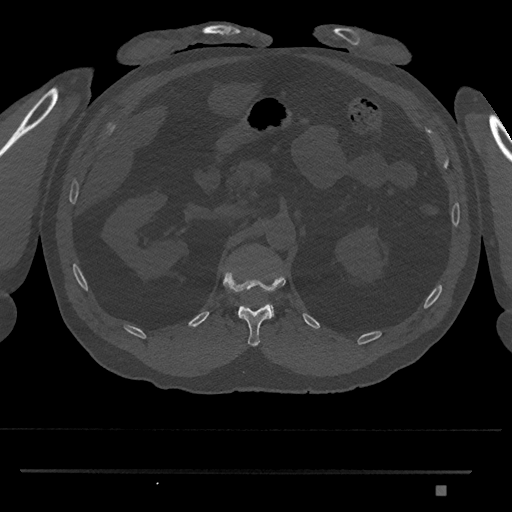
CT including the spine, one axial slice; position 867 of 1134 along the scan axis; reconstruction kernel Br40s/3; bone window (W 1800 / L 400 HU); 0.5 mm slice thickness; 512 × 512 image matrix, field of view 429 × 429 mm. Patient: male, 65 years. Case-level facts recorded for this patient, not image findings: primary cancer: prostate.
Annotated regions visible in this slice (semi-automatically segmented with operator editing):
- L1 vertebra: box from (x=270, y=305) to (x=274, y=318) px
- T12 vertebra: (x=223, y=266)–(x=286, y=347)